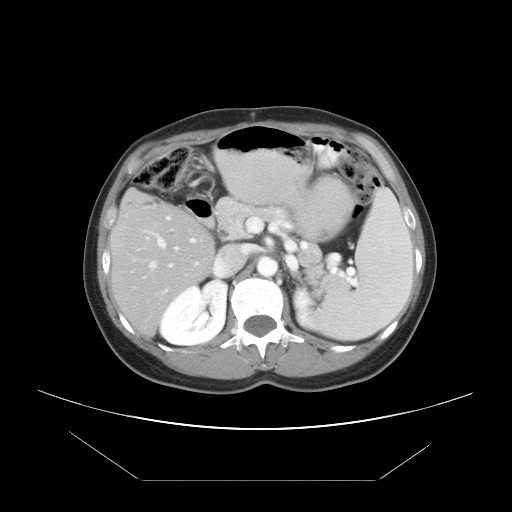
Contrast-enhanced abdominal CT, one axial slice; slice 24 of 45 in the series (ordered by position); reconstruction kernel STANDARD; intravenous contrast given; soft-tissue window (W 400 / L 40 HU); 5 mm slice thickness; 512 × 512 image matrix. Female patient, age 52 years. Case-level facts recorded for this patient, not image findings: diagnosis: colorectal cancer liver metastases, imaged before liver resection; multiple liver metastases: yes; largest metastasis: 2.5 cm; disease in both lobes: no.
Structures marked on this image (manually delineated by an expert):
- hepatic veins: box from (x=150, y=239) to (x=173, y=268) px
- liver: (x=112, y=193)–(x=212, y=333)
- planned liver remnant (the part of the liver to remain after resection): (x=112, y=194)–(x=212, y=333)
- portal vein (with intrahepatic branches): (x=146, y=216)–(x=197, y=293)